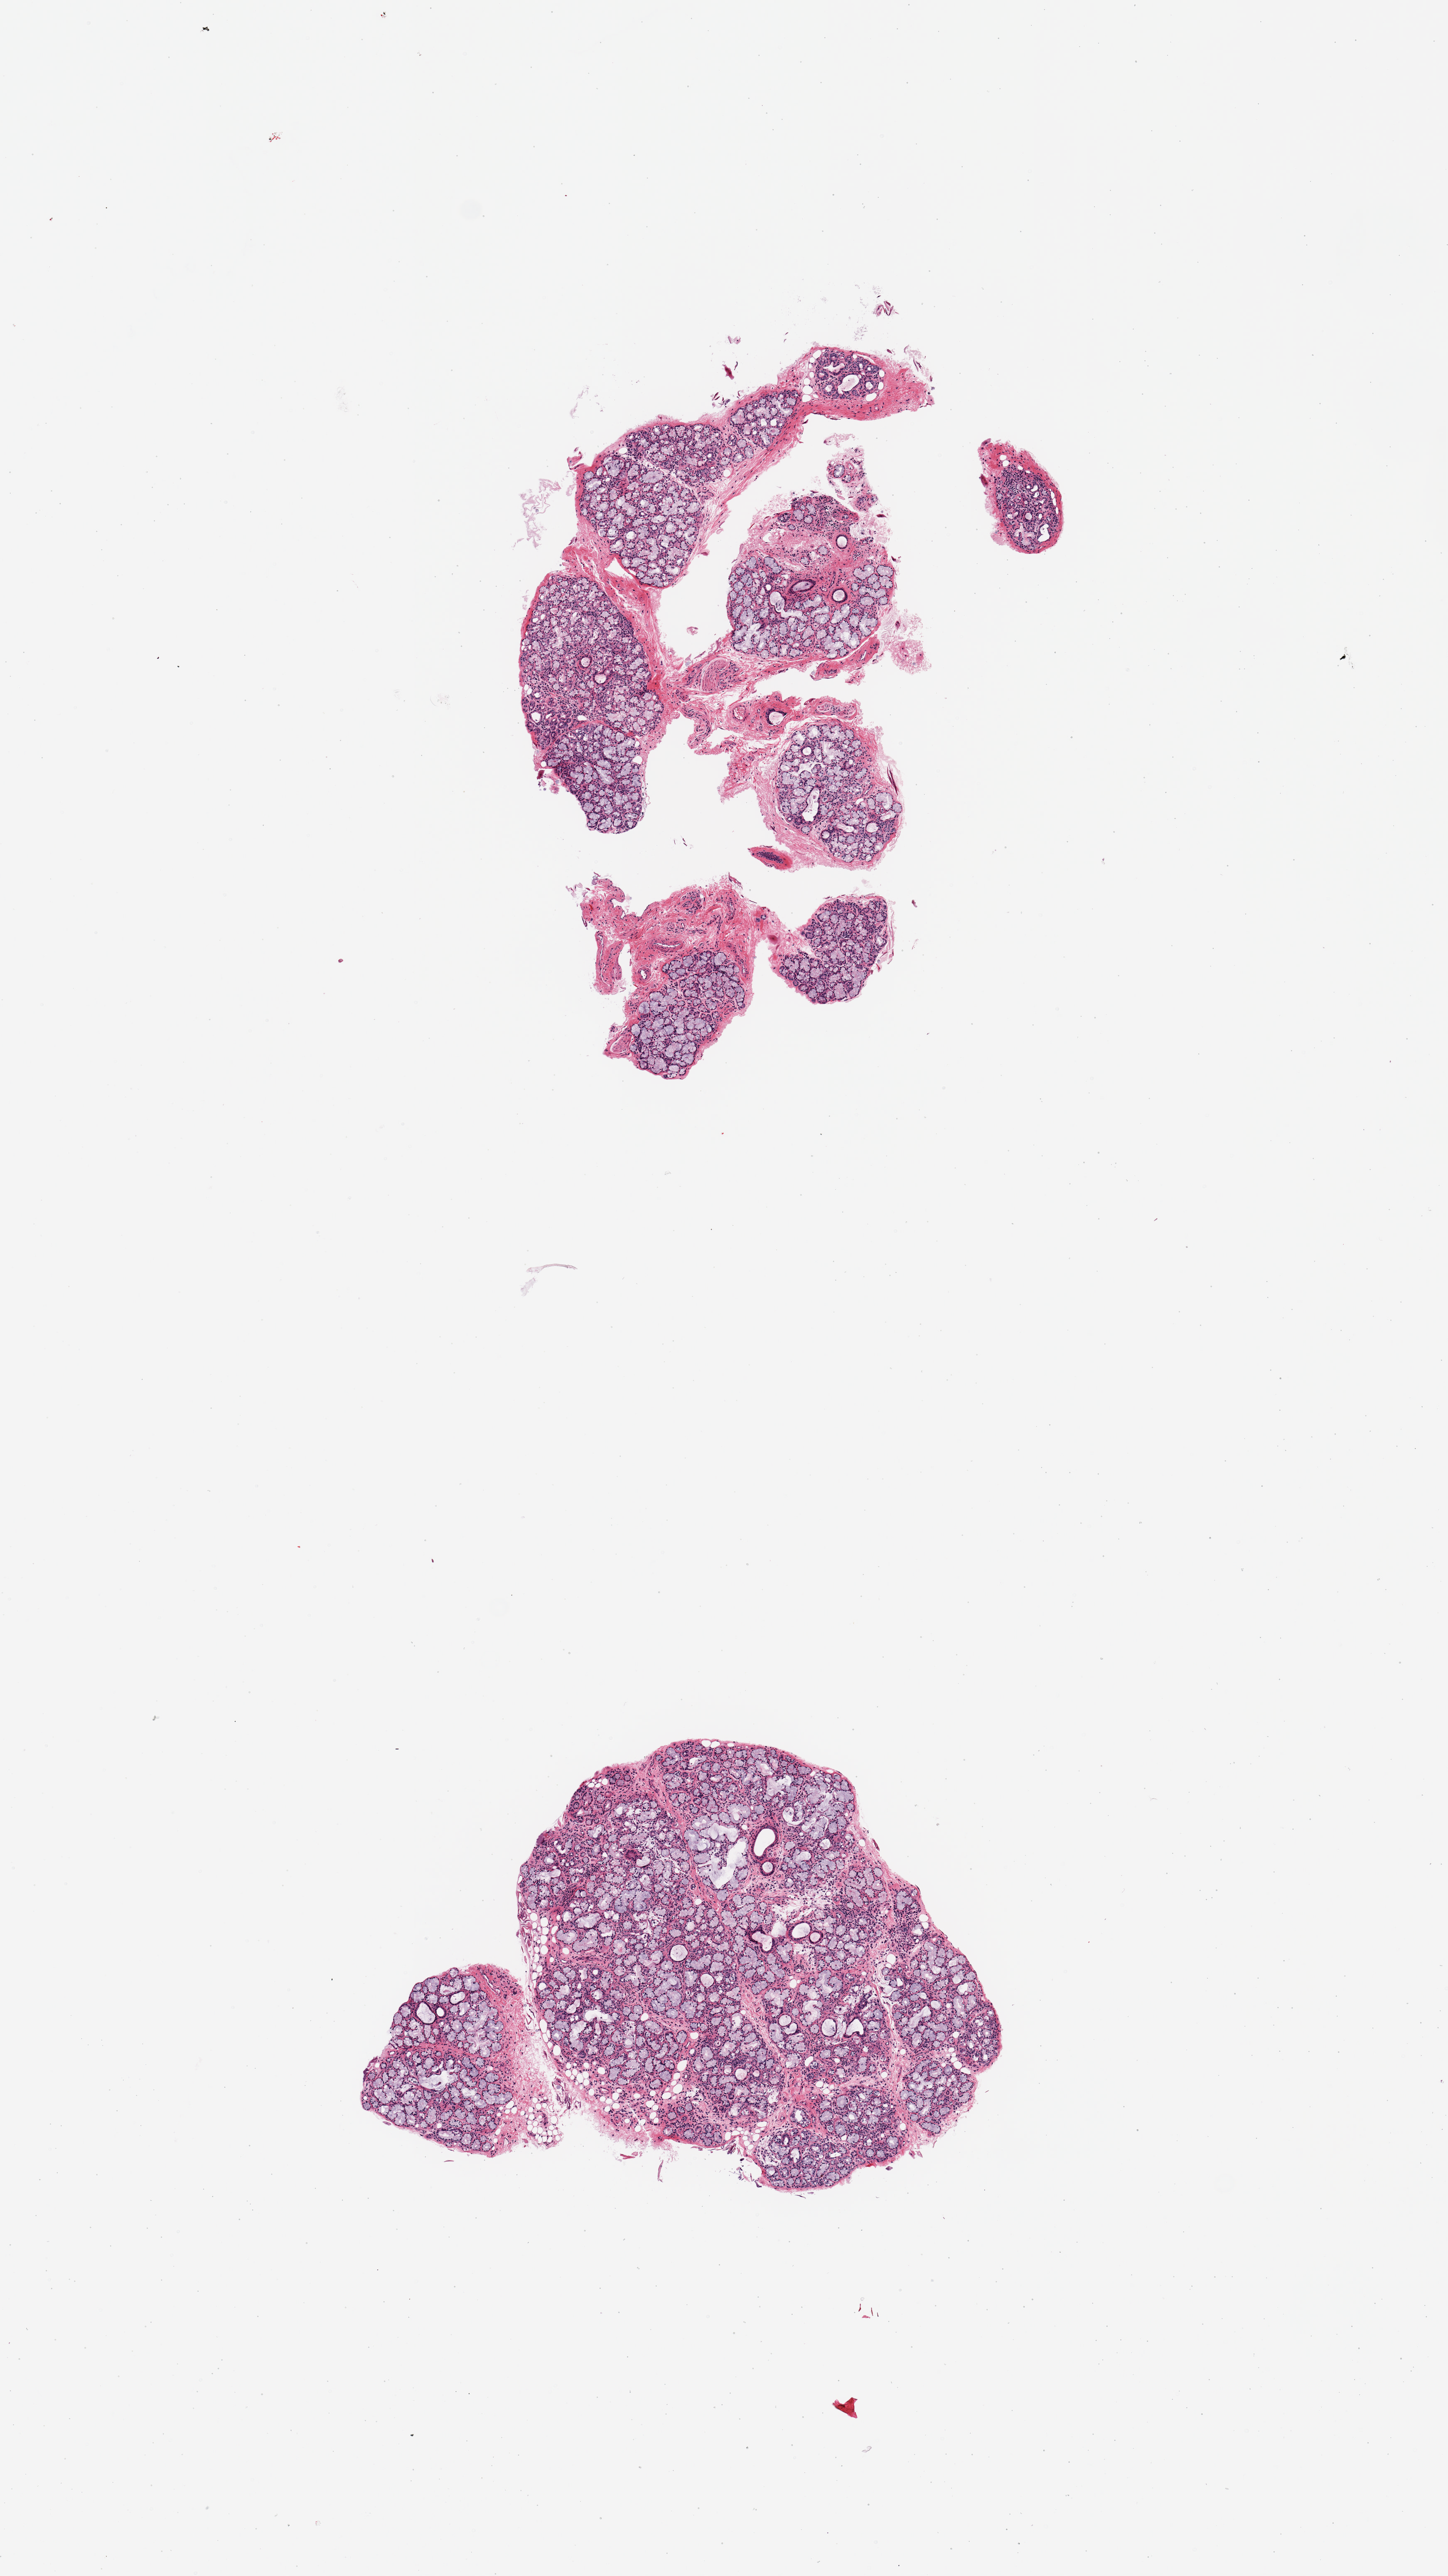
Digitized H&E-stained section, a low-resolution overview of the entire scanned area, about 6.9 x 12.3 mm (from a 20x scan); PAXgene-fixed, paraffin-embedded tissue; target tissue: minor salivary gland; donor tissue sample. Donor: male.
* review note (as recorded): 2 pieces, ~99% glandular elements; good specimen